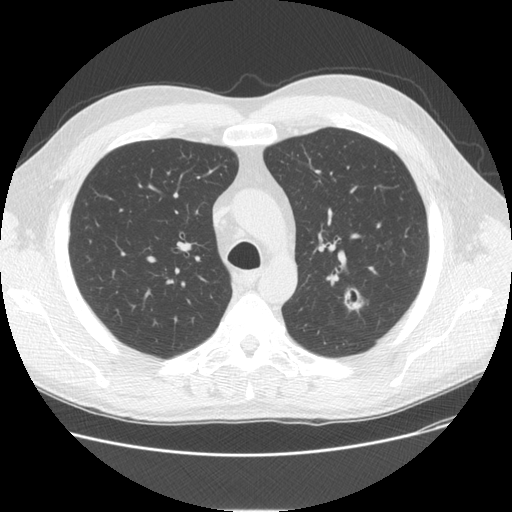
Low-dose screening chest CT, one axial slice. Position 112 of 150 along the scan axis. Reconstruction kernel STANDARD. Lung window (W 1500 / L -600 HU). 2.5 mm slice thickness. 512 × 512 image matrix, field of view 370 × 370 mm.
Structures marked on this image (outlined manually by an expert reader):
- lesion 1 (tumor, upper lobe of left lung): bounding box <345,289,363,310> (left, top, right, bottom; pixels)